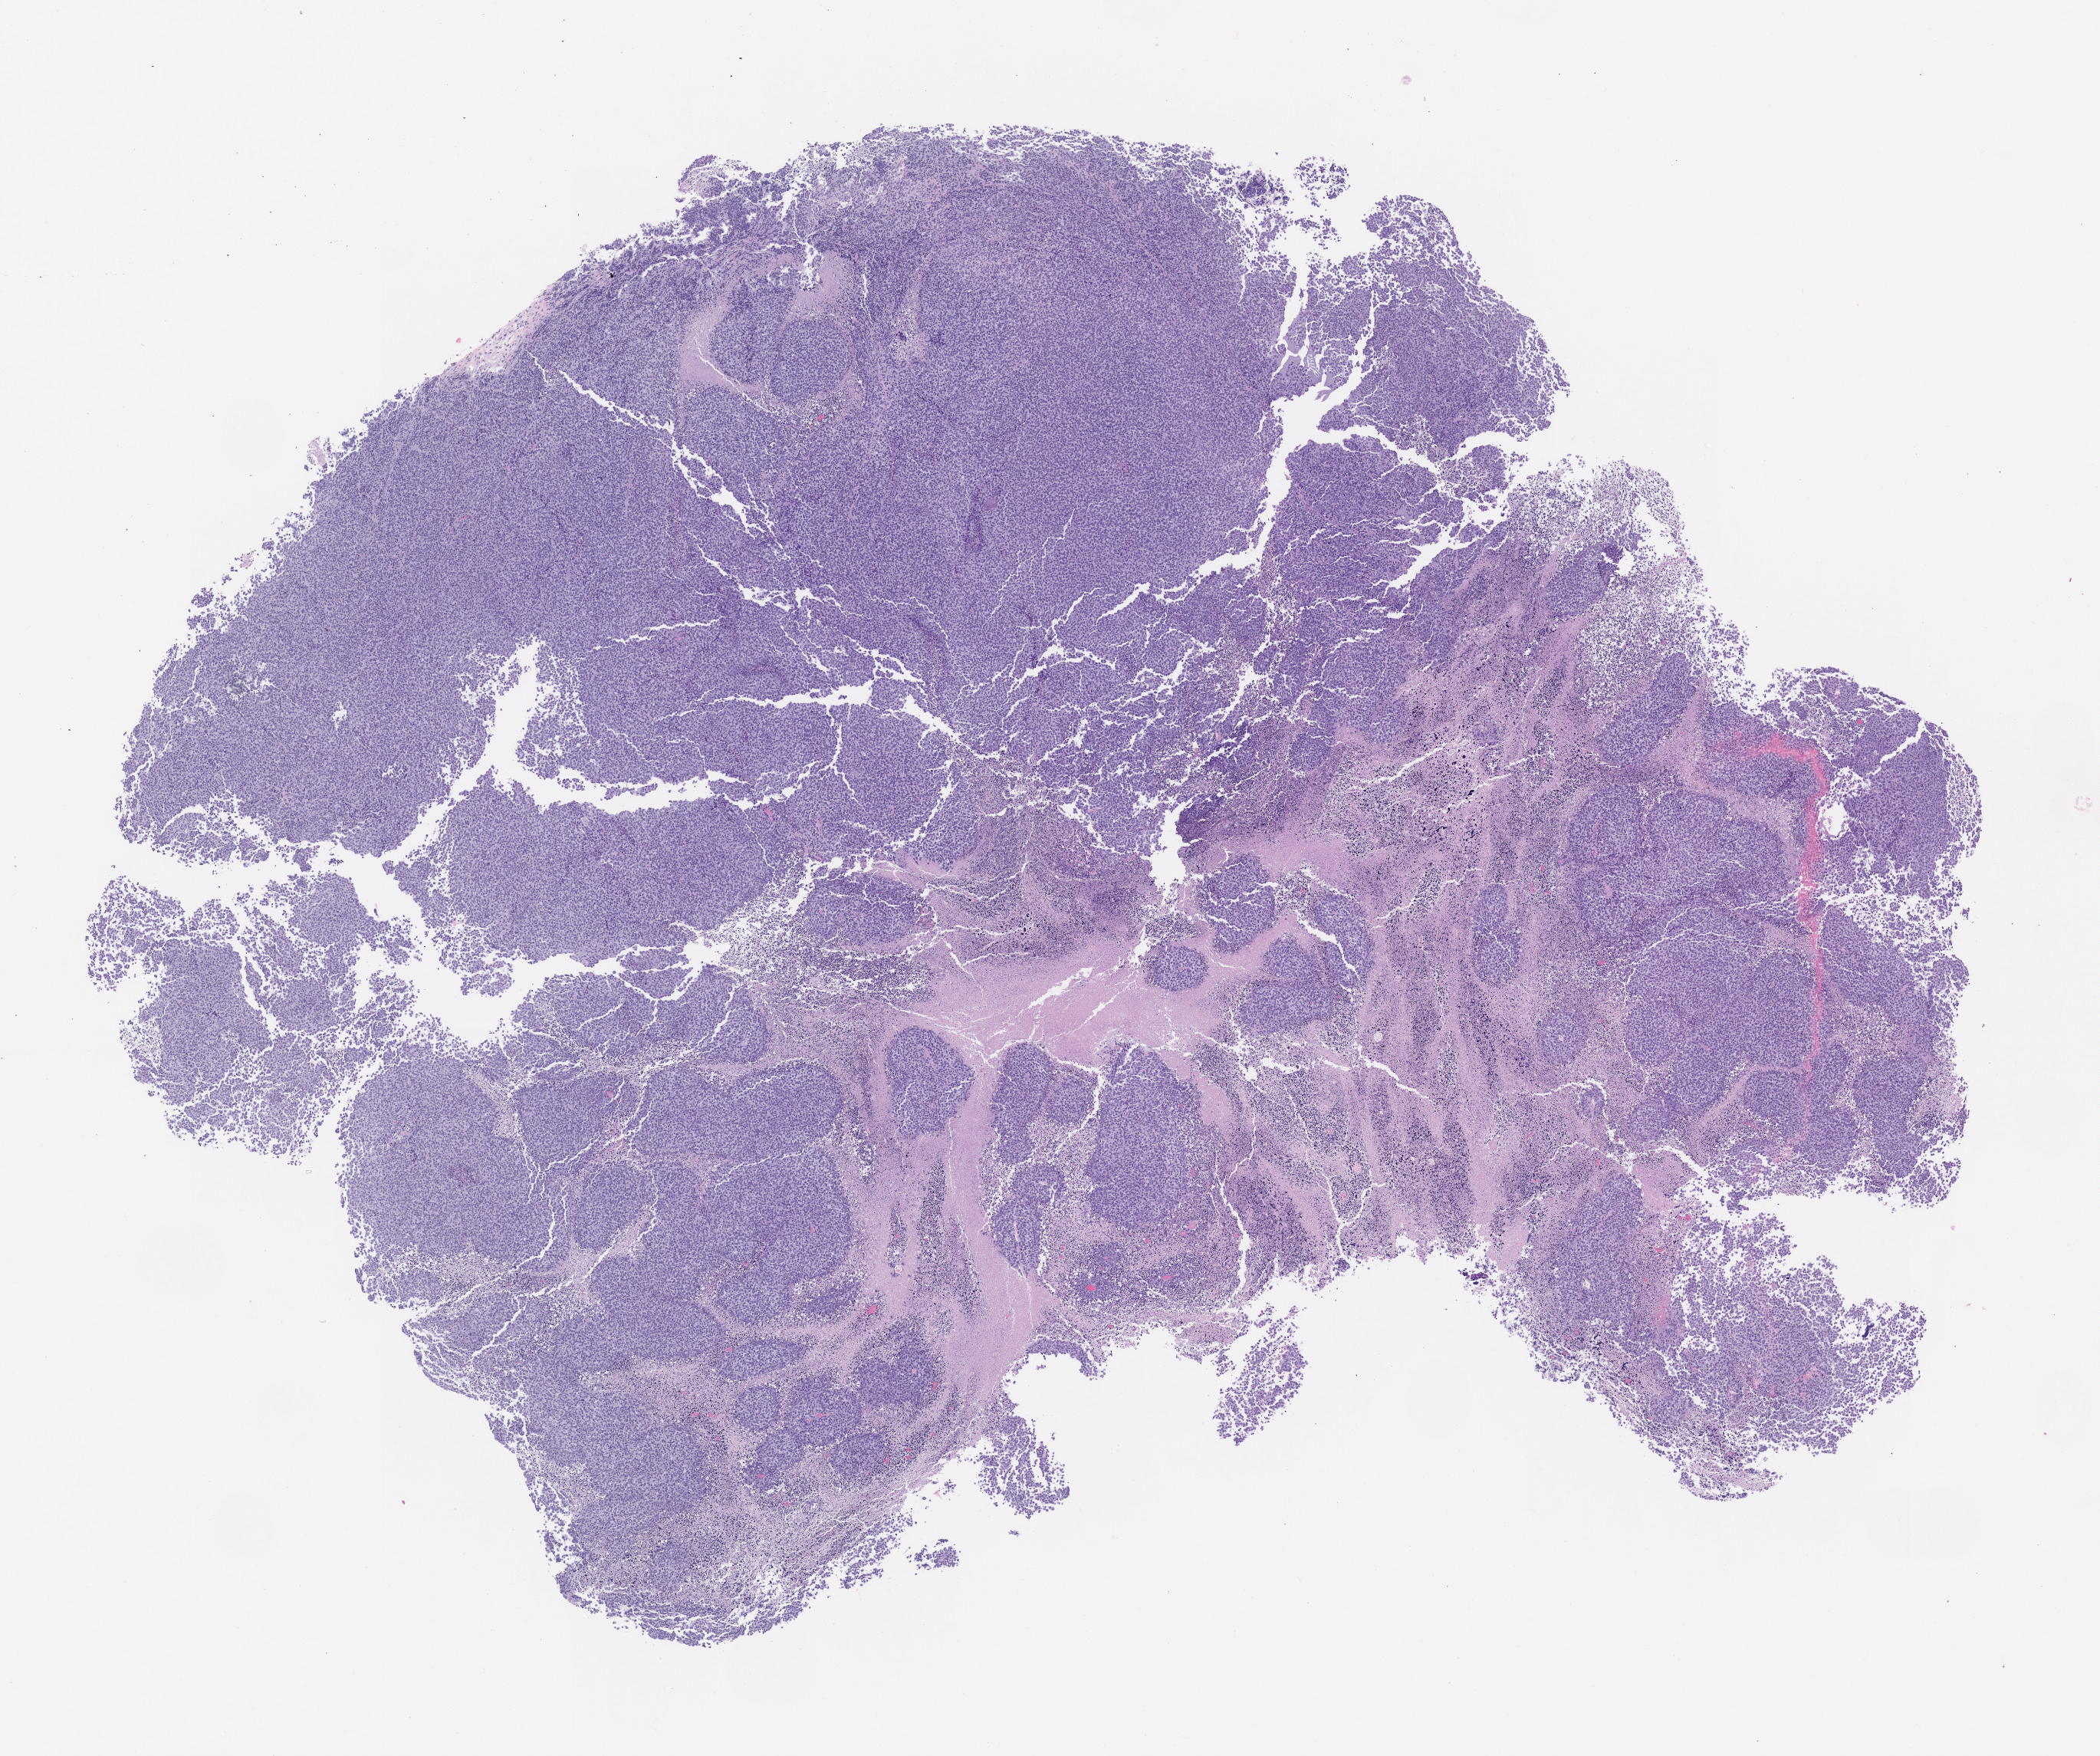
Whole-slide image, H&E: patient-derived xenograft (human tumor grown in a mouse), passage 0 — low-resolution overview of the scanned area, about 11.0 x 9.2 mm; formalin-fixed paraffin-embedded section; tumor site category: musculoskeletal.
Originating patient diagnosis: Ewing Sarcoma|Primitive Neuroectodermal Tumor.